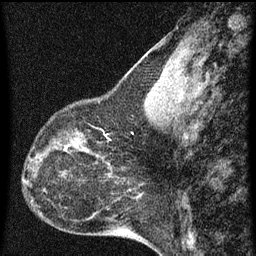
Breast MRI (dynamic contrast-enhanced), one sagittal slice. Slice 25 of 60 in the series (ordered by position). Dynamic contrast-enhanced series, image 2 of 3 at this slice position (ordered by acquisition). 1.5 T. TE 4.2 ms, TR 8 ms. 2 mm slice thickness. 256 × 256 image matrix, field of view 180 × 180 mm. Patient: female, 44 years.
Annotated regions visible in this slice (semi-automatically segmented with operator editing):
- analysis volume of interest (the breast-tissue region the enhancement analysis was run in; not a lesion): bounding box (x1, y1, x2, y2) in pixels: (49, 128, 95, 169)
- tumour enhancement mask (voxels above the 70 % enhancement threshold inside the analysis volume of interest): (76, 134, 92, 155)